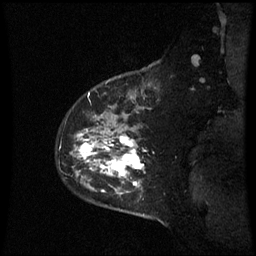
Breast MRI (dynamic contrast-enhanced), one sagittal slice; position 49 of 60 along the scan axis; dynamic contrast-enhanced series, image 2 of 3 at this slice position (ordered by acquisition); 1.5 T; TE 4.2 ms, TR 8.9 ms; 256 × 256 image matrix, field of view 210 × 210 mm. Patient: female, 43 years. Case-level facts recorded for this patient, not image findings: setting: breast cancer imaged before/during neoadjuvant chemotherapy; receptor status: HER2-positive.
Structures marked on this image (semi-automatic segmentation, software-assisted and operator-edited):
- analysis volume of interest (the breast-tissue region the enhancement analysis was run in; not a lesion): bounding box (x1, y1, x2, y2) in pixels: (61, 80, 155, 195)
- tumour enhancement mask (voxels above the 70 % enhancement threshold inside the analysis volume of interest): (79, 137, 145, 193)